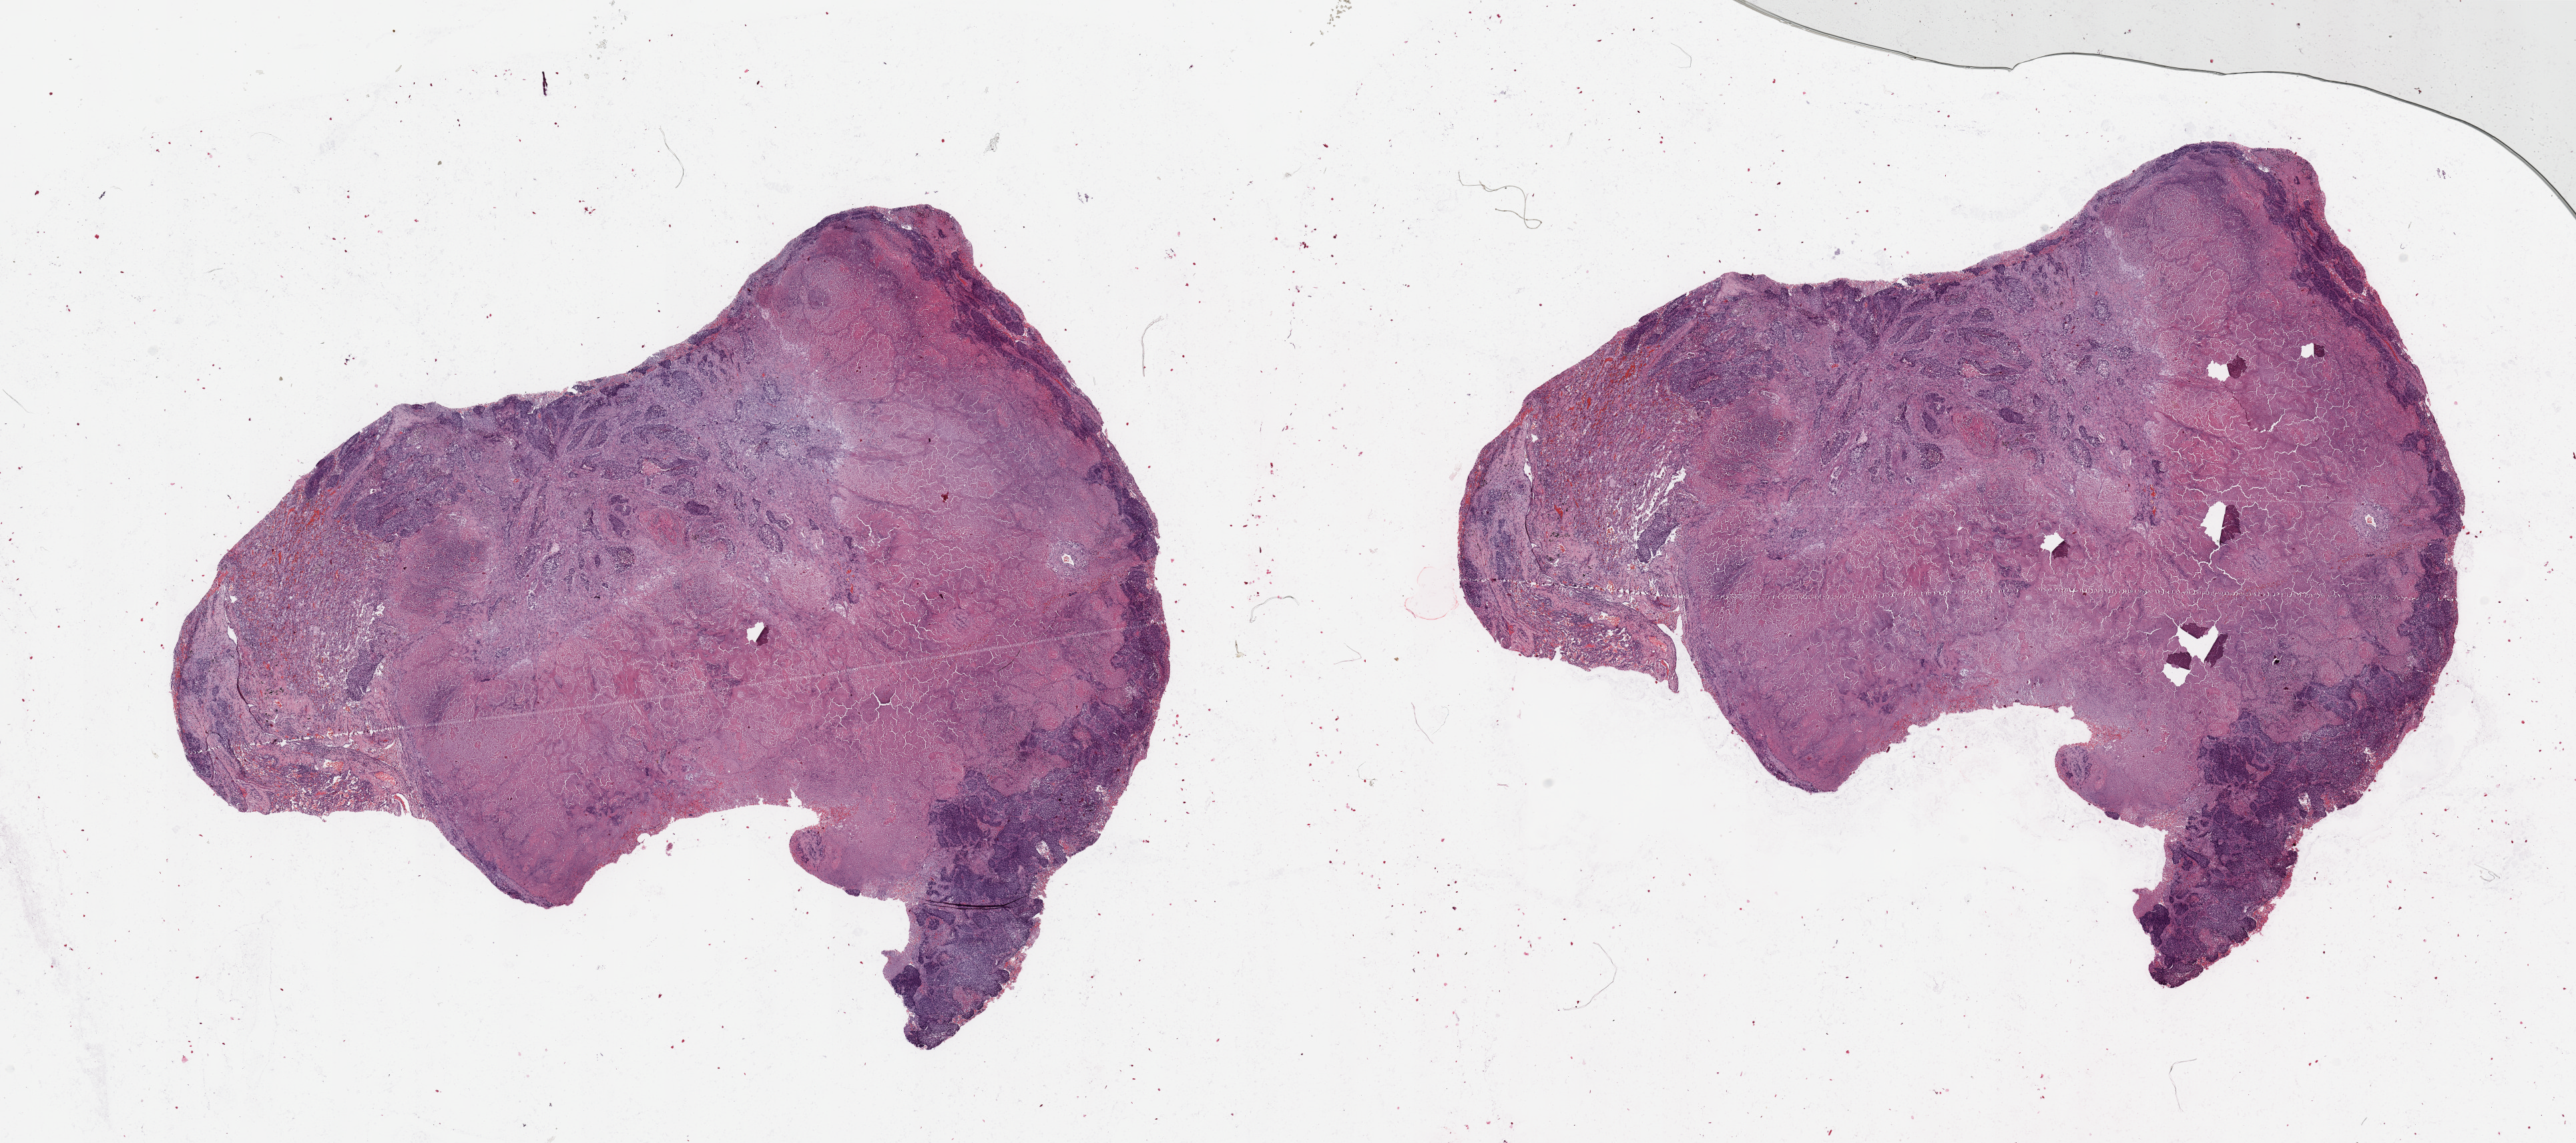
H&E whole-slide image, whole scanned area (about 30.5 x 13.5 mm, from a 20x scan) shown as a low-resolution overview. Lung, tumour tissue. Patient: male, age 54 years. Histologic grade: G2 (moderately differentiated).
AJCC pathologic stage: IIIA. Histologic diagnosis: Squamous cell carcinoma, NOS.